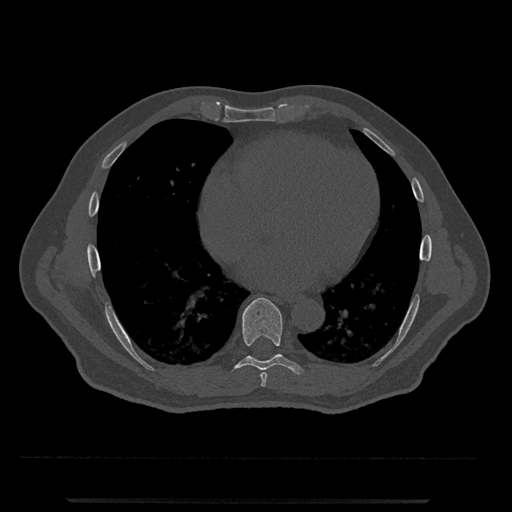
CT including the spine, one axial slice; slice 628 of 797 in the series (ordered by position); bone window (W 1800 / L 400 HU); 0.5 mm slice thickness; 512 × 512 image matrix, field of view 419 × 419 mm. Male patient, age 63 years. From the clinical record (not read from this slice): primary cancer: prostate.
Outlined on this slice (semi-automatically segmented with operator editing):
- T7 vertebra: bounding box (x1, y1, x2, y2) in pixels: (260, 372, 267, 387)
- T8 vertebra: (233, 298, 304, 374)